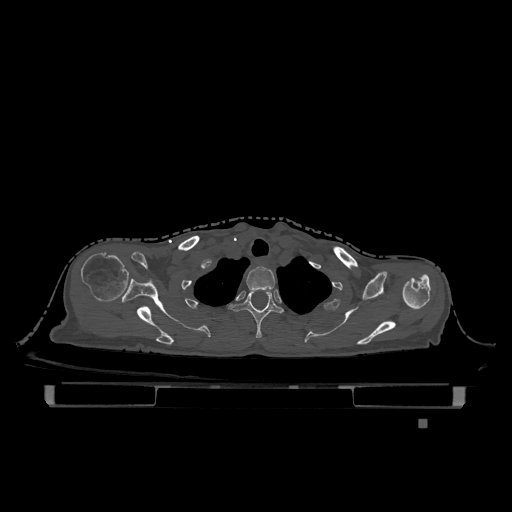
CT including the spine, one axial slice; bone window (W 1800 / L 400 HU); 0.5 mm slice thickness; 512 × 512 image matrix, field of view 500 × 500 mm. Patient: female, 74 years. From the clinical record (not read from this slice): primary cancer: lung; vertebrae with lytic lesions (as recorded): T1, T4, T5, T6, L4, L5.
Structures marked on this image (semi-automatically segmented with operator editing):
- T1 vertebra: bounding box <246,266,276,291> (left, top, right, bottom; pixels)
- T2 vertebra: <229,290,283,338>